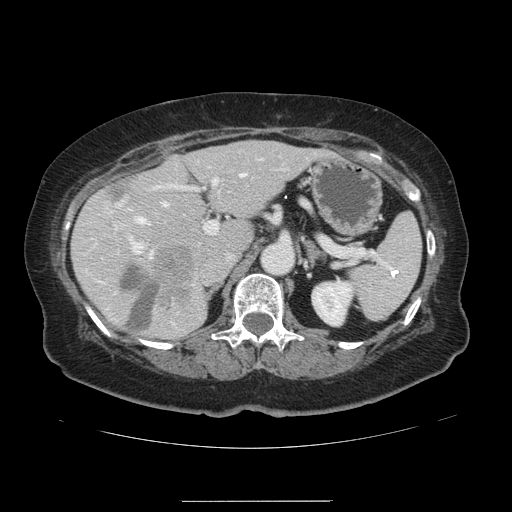
Contrast-enhanced abdominal CT, one axial slice; slice 79 of 141 in the series (ordered by position); intravenous contrast given; soft-tissue window (W 400 / L 40 HU); 2.5 mm slice thickness; 512 × 512 image matrix, field of view 393 × 393 mm. Female patient, age 74 years. Case-level facts recorded for this patient, not image findings: diagnosis: colorectal cancer liver metastases, imaged before liver resection; multiple liver metastases: yes; largest metastasis: 7 cm; disease in both lobes: yes.
Annotated regions visible in this slice (manually delineated by an expert):
- hepatic veins: bounding box [x1, y1, x2, y2] px = [132, 173, 245, 226]
- liver: [73, 141, 323, 341]
- planned liver remnant (the part of the liver to remain after resection): [74, 141, 323, 340]
- portal vein (with intrahepatic branches): [129, 158, 261, 258]
- liver metastasis: [105, 180, 133, 204]
- liver metastasis: [121, 266, 161, 333]
- liver metastasis: [145, 243, 194, 303]